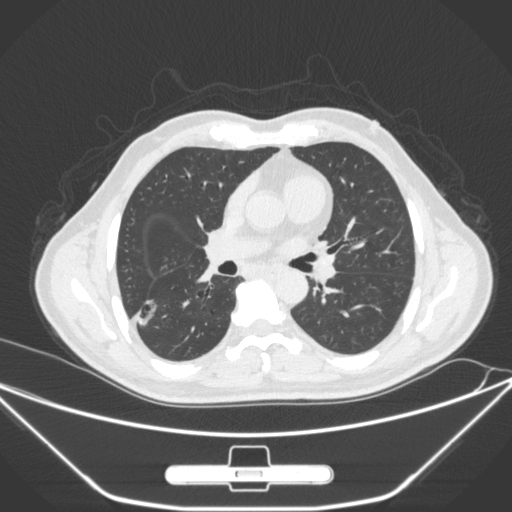
Chest CT, one axial slice; slice 156 of 310 in the series (ordered by position); 120 kVp; lung window (W 1500 / L -600 HU); 1 mm slice thickness; 512 × 512 image matrix, field of view 398 × 398 mm. Patient: male, 71 years. From the clinical record (not read from this slice): clinical TNM (as recorded): T1c N0 M0; histopathological grade: G2.
Structures marked on this image (rectangle marked by the reading radiologist):
- lung tumour (recorded histology: adenocarcinoma): box from (x=133, y=294) to (x=160, y=329) px